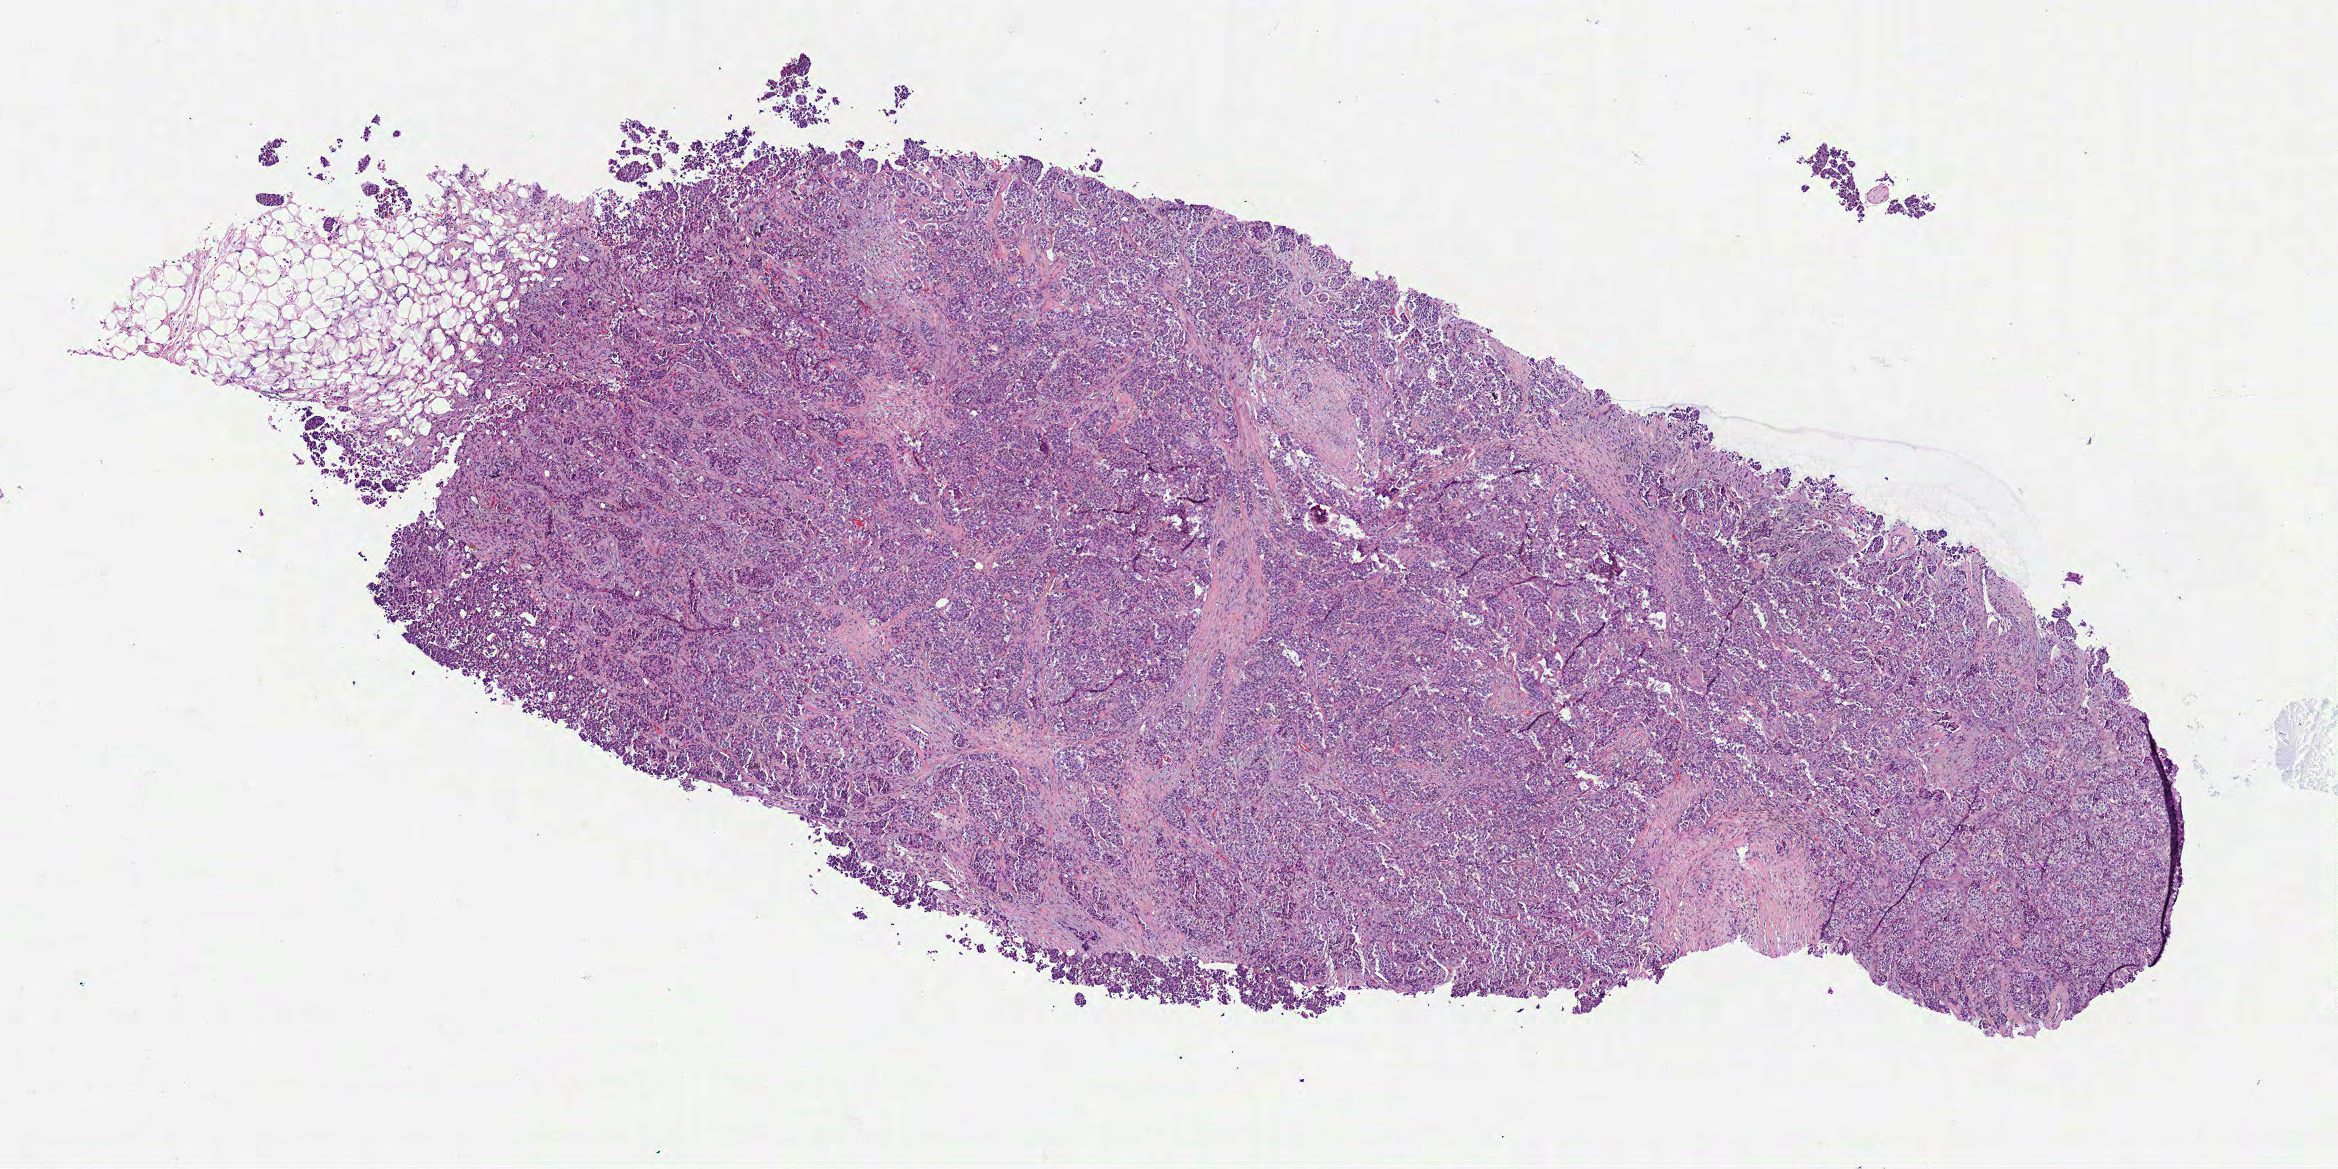
Digitized H&E-stained tissue section (whole slide) — a low-resolution overview of the entire scanned area, about 9.4 x 4.7 mm (from a 40x scan); formalin-fixed paraffin-embedded (FFPE) diagnostic section; primary tumour sample from the breast. Male patient; age at initial diagnosis 58 years.
Pathologic diagnosis: Infiltrating duct carcinoma, NOS. AJCC pathologic stage: IV (7th edition). Laterality: right. Lymph nodes positive (case pathology): 3 of 17 examined.